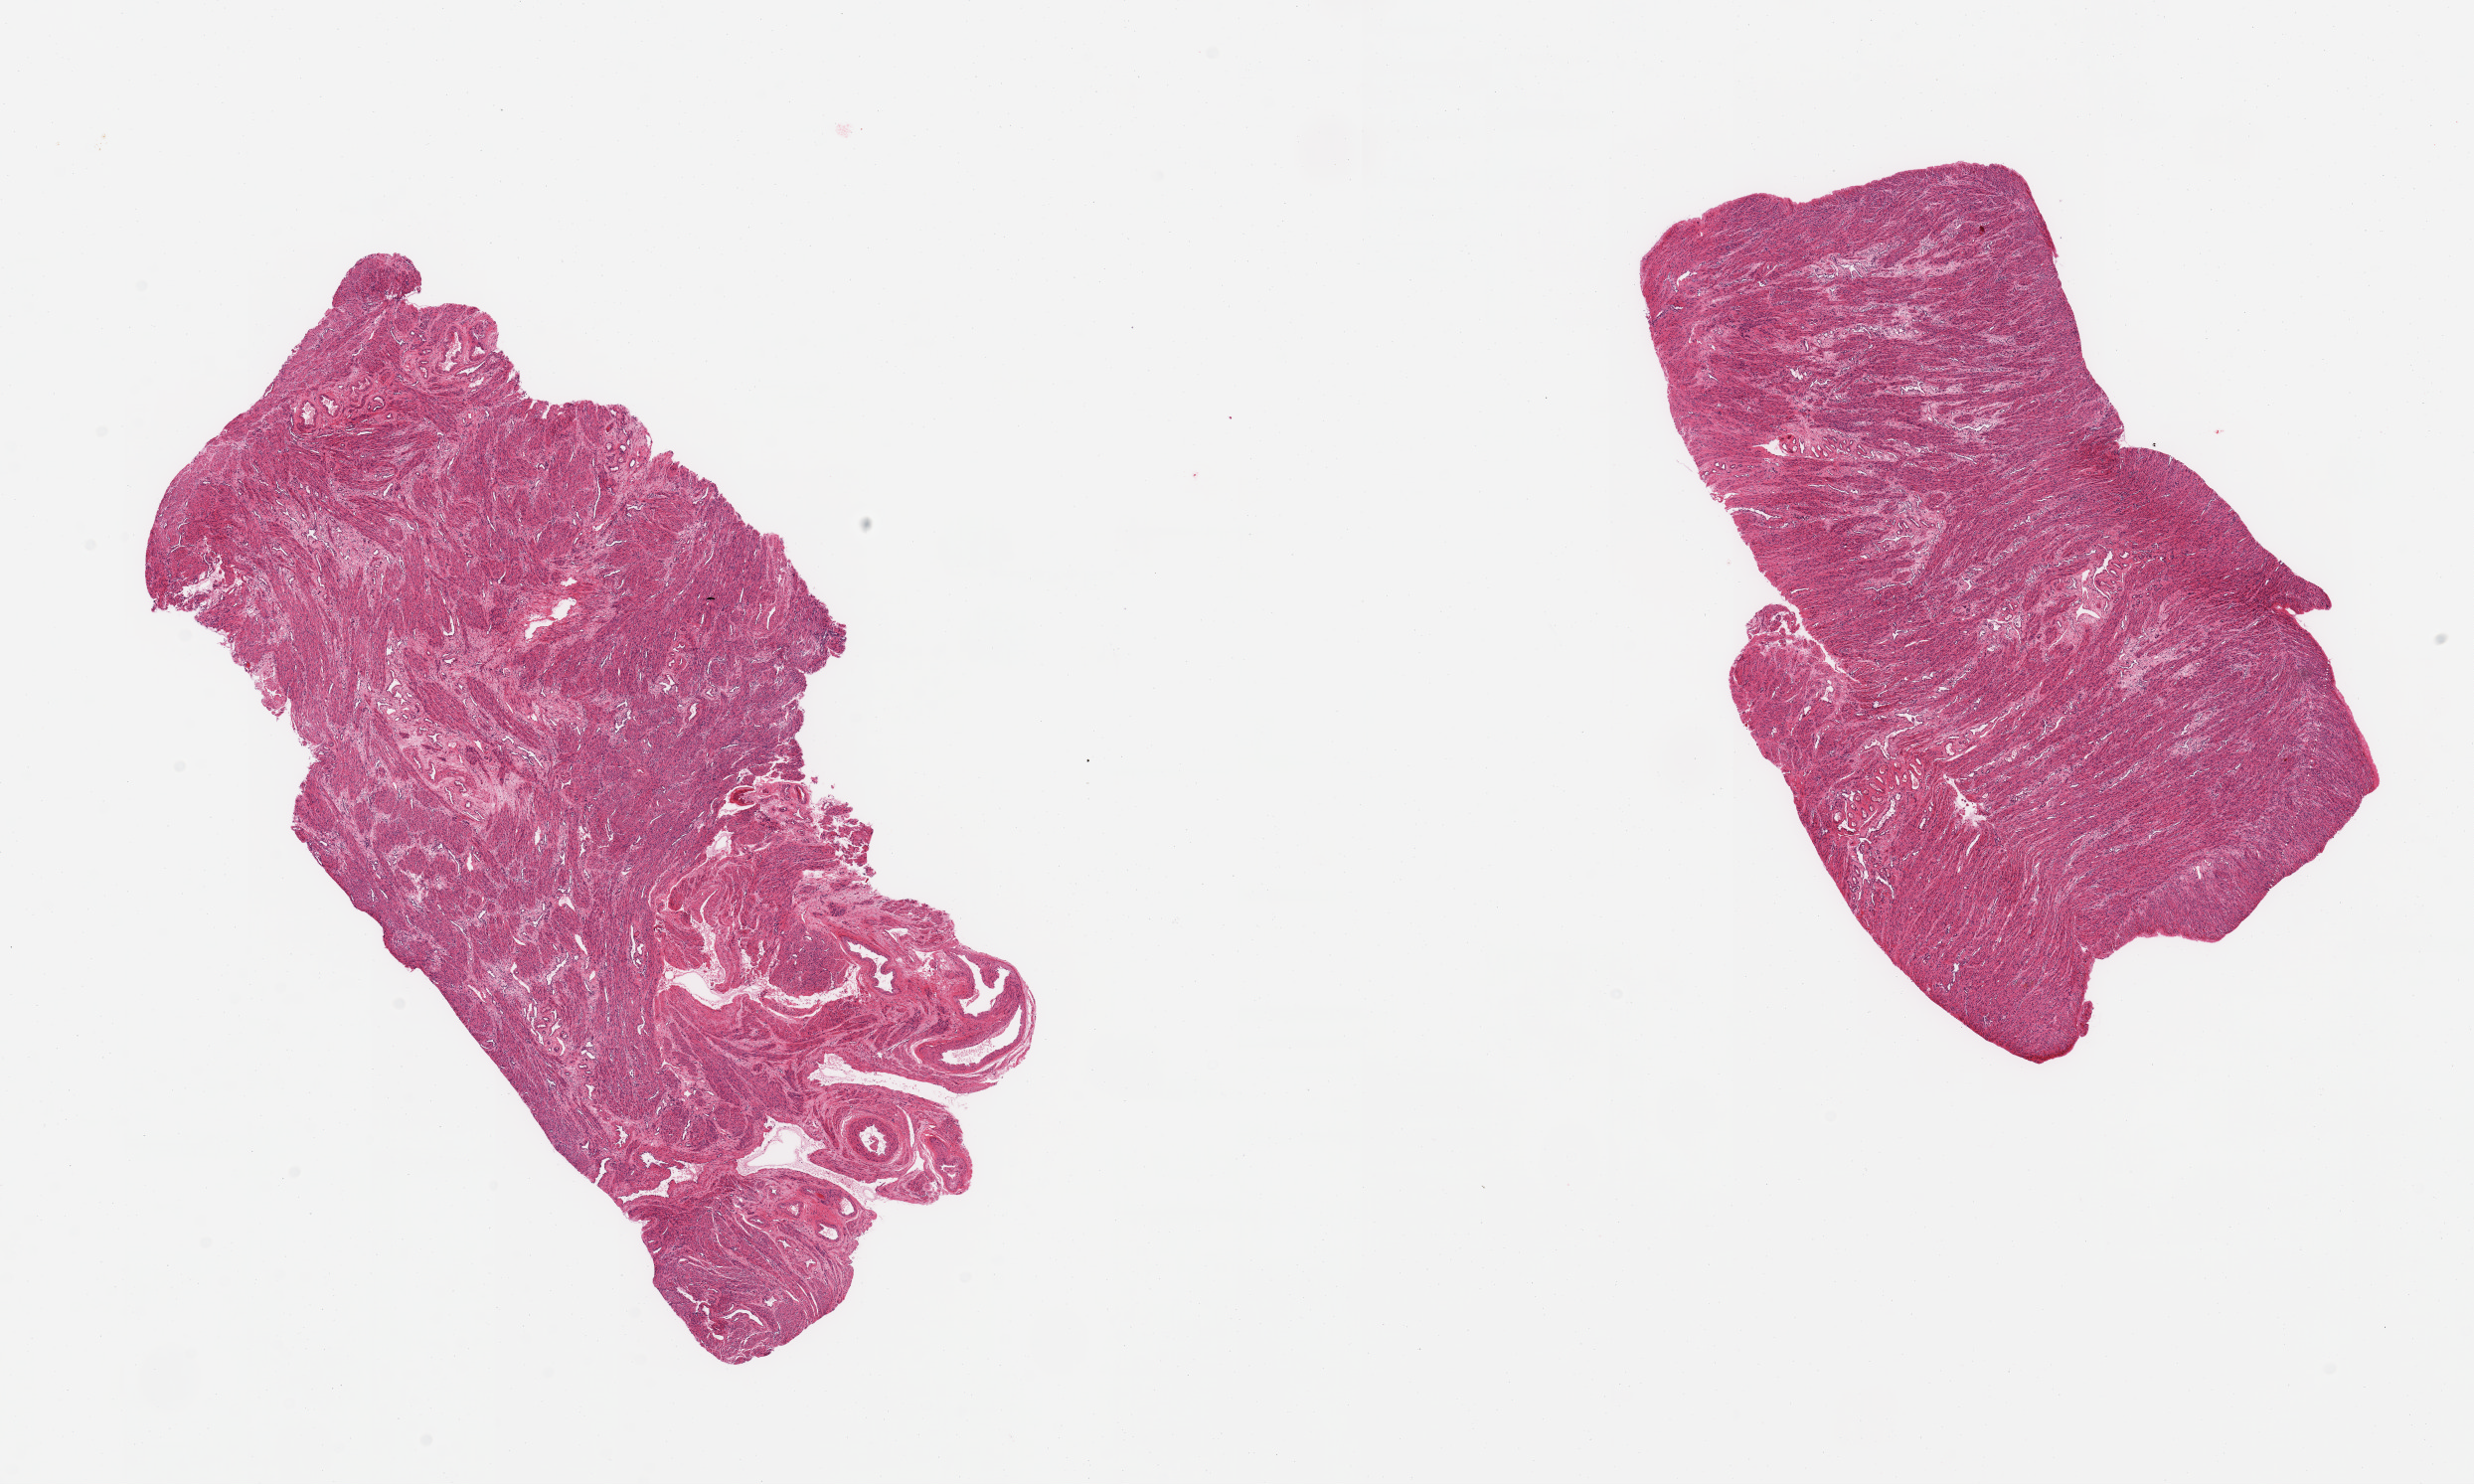
Haematoxylin and eosin whole-slide image, brightfield, whole scanned area (about 19.7 x 11.8 mm) shown as a low-resolution overview, PAXgene-fixed, paraffin-embedded tissue, section of uterus (target tissue), tissue donor sample. Donor: female.
Review note (as recorded): 2 pieces, myometrium only.